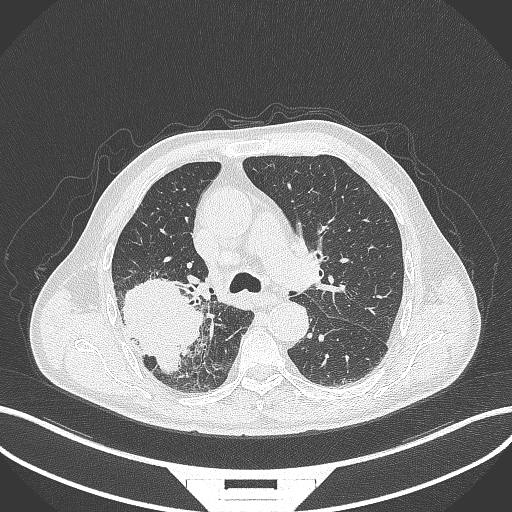
Chest CT, one axial slice; slice 266 of 429 in the series (ordered by position); reconstruction kernel B70f; 120 kVp; lung window (W 1500 / L -600 HU); 1 mm slice thickness; 512 × 512 image matrix, field of view 400 × 400 mm. Male patient, age 72 years. From the clinical record (not read from this slice): clinical TNM (as recorded): T3 N2 M0.
Structures marked on this image (rectangle marked by the reading radiologist):
- lung tumour (recorded histology: adenocarcinoma): bounding box (x1, y1, x2, y2) in pixels: (116, 274, 208, 375)